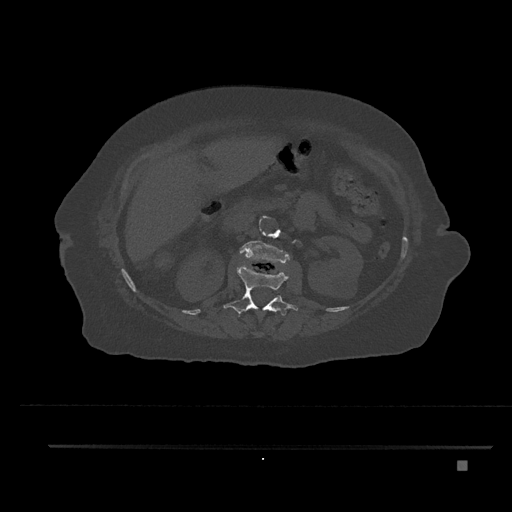
CT including the spine, one axial slice; slice 215 of 797 in the series (ordered by position); 120 kVp; bone window (W 1800 / L 400 HU); 0.5 mm slice thickness; 512 × 512 image matrix, field of view 437 × 437 mm. Female patient, age 76 years. From the clinical record (not read from this slice): primary cancer: lung; vertebrae with lytic lesions (as recorded): T11, L3.
Outlined on this slice (semi-automatic segmentation, software-assisted and operator-edited):
- L1 vertebra: bounding box <223,265,298,318> (left, top, right, bottom; pixels)
- L2 vertebra: <240,240,290,263>
- T12 vertebra: <257,311,275,337>